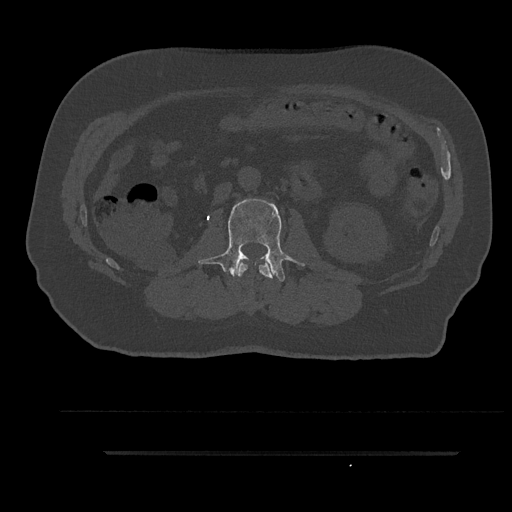
CT including the spine, one axial slice. Position 120 of 797 along the scan axis. Bone window (W 1800 / L 400 HU). 0.5 mm slice thickness. 512 × 512 image matrix, field of view 432 × 432 mm. Patient: male, 63 years. From the clinical record (not read from this slice): primary cancer: renal.
Outlined on this slice (semi-automatic segmentation, software-assisted and operator-edited):
- L1 vertebra: bounding box (x1, y1, x2, y2) in pixels: (238, 259, 274, 279)
- L2 vertebra: (198, 199, 305, 282)